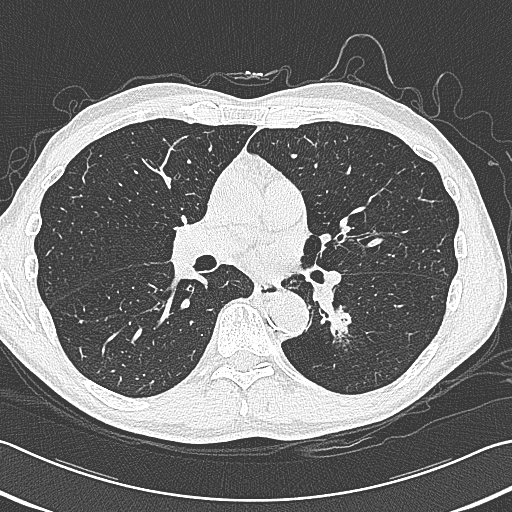
Axial slice from a low-dose chest CT screening exam. First (baseline) screen. Lung window (W 1500 / L -600 HU). 1 mm slice thickness. 120 kVp. 512 × 512 image matrix. Male participant, aged 59 years at enrolment. Former smoker at enrolment.
Lesion marked by an expert reader, bounding box (x1, y1, x2, y2) in pixels: (314, 293, 375, 353). Reader record for this screening exam (exam-level; its link to the box is not recorded): non-calcified nodule or mass ≥4 mm, left lower lobe, 15 × 15 mm, smooth margins, soft tissue attenuation. Official screen result: positive, change unspecified: nodule(s) >= 4 mm or enlarging nodule(s), mass(es), or other non-specific abnormalities suspicious for lung cancer. Later outcome: lung cancer diagnosed 17 days after this screen — squamous cell carcinoma, large cell, nonkeratinizing, NOS, left lower lobe, poorly differentiated (G3), stage IB (AJCC 6th edition), 31 mm at pathology.